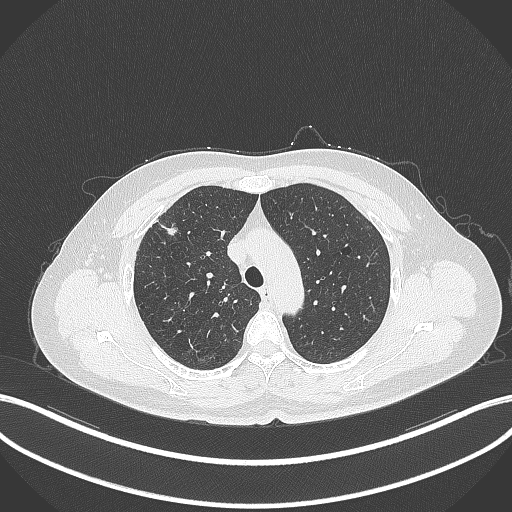
Chest CT, one axial slice. Position 272 of 353 along the scan axis. Lung window (W 1500 / L -600 HU). 1 mm slice thickness. 512 × 512 image matrix, field of view 400 × 400 mm. Patient: female, 56 years. From the clinical record (not read from this slice): clinical TNM (as recorded): T1c N0 M0.
Structures marked on this image (bounding box drawn by a radiologist):
- lung tumour (recorded histology: adenocarcinoma): bounding box [x1, y1, x2, y2] px = [157, 220, 179, 240]